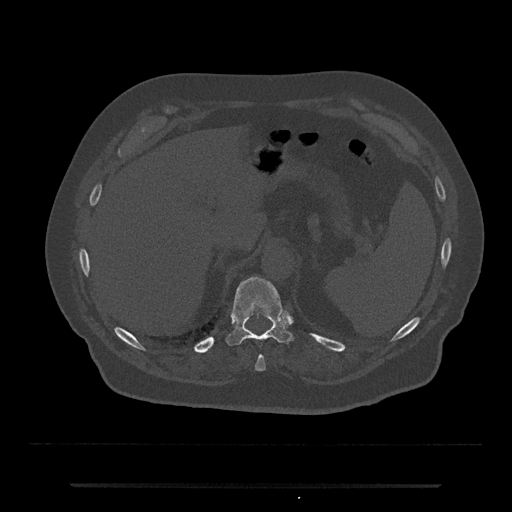
CT including the spine, one axial slice. Position 658 of 797 along the scan axis. Reconstruction kernel Br40s/3. 120 kVp. Bone window (W 1800 / L 400 HU). 0.5 mm slice thickness. 512 × 512 image matrix, field of view 434 × 434 mm. Male patient, age 80 years. Case-level facts recorded for this patient, not image findings: primary cancer: prostate.
Structures marked on this image (semi-automatically segmented with operator editing):
- T10 vertebra: bounding box [x1, y1, x2, y2] px = [255, 355, 266, 371]
- T11 vertebra: [226, 277, 293, 346]